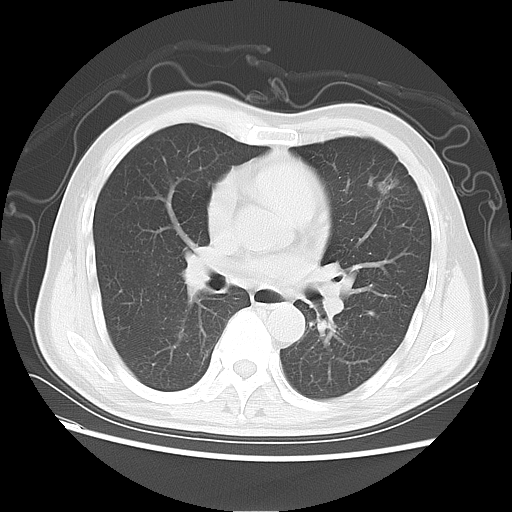
Chest CT, one axial slice. Slice 34 of 64 in the series (ordered by position). 120 kVp. Lung window (W 1500 / L -600 HU). 5 mm slice thickness. 512 × 512 image matrix, field of view 368 × 368 mm. Patient: male, 60 years. Case-level facts recorded for this patient, not image findings: clinical TNM (as recorded): T2a N0 M0; histopathological grade: G3.
Outlined on this slice (rectangle marked by the reading radiologist):
- lung tumour (recorded histology: adenocarcinoma): bounding box <371,169,408,208> (left, top, right, bottom; pixels)